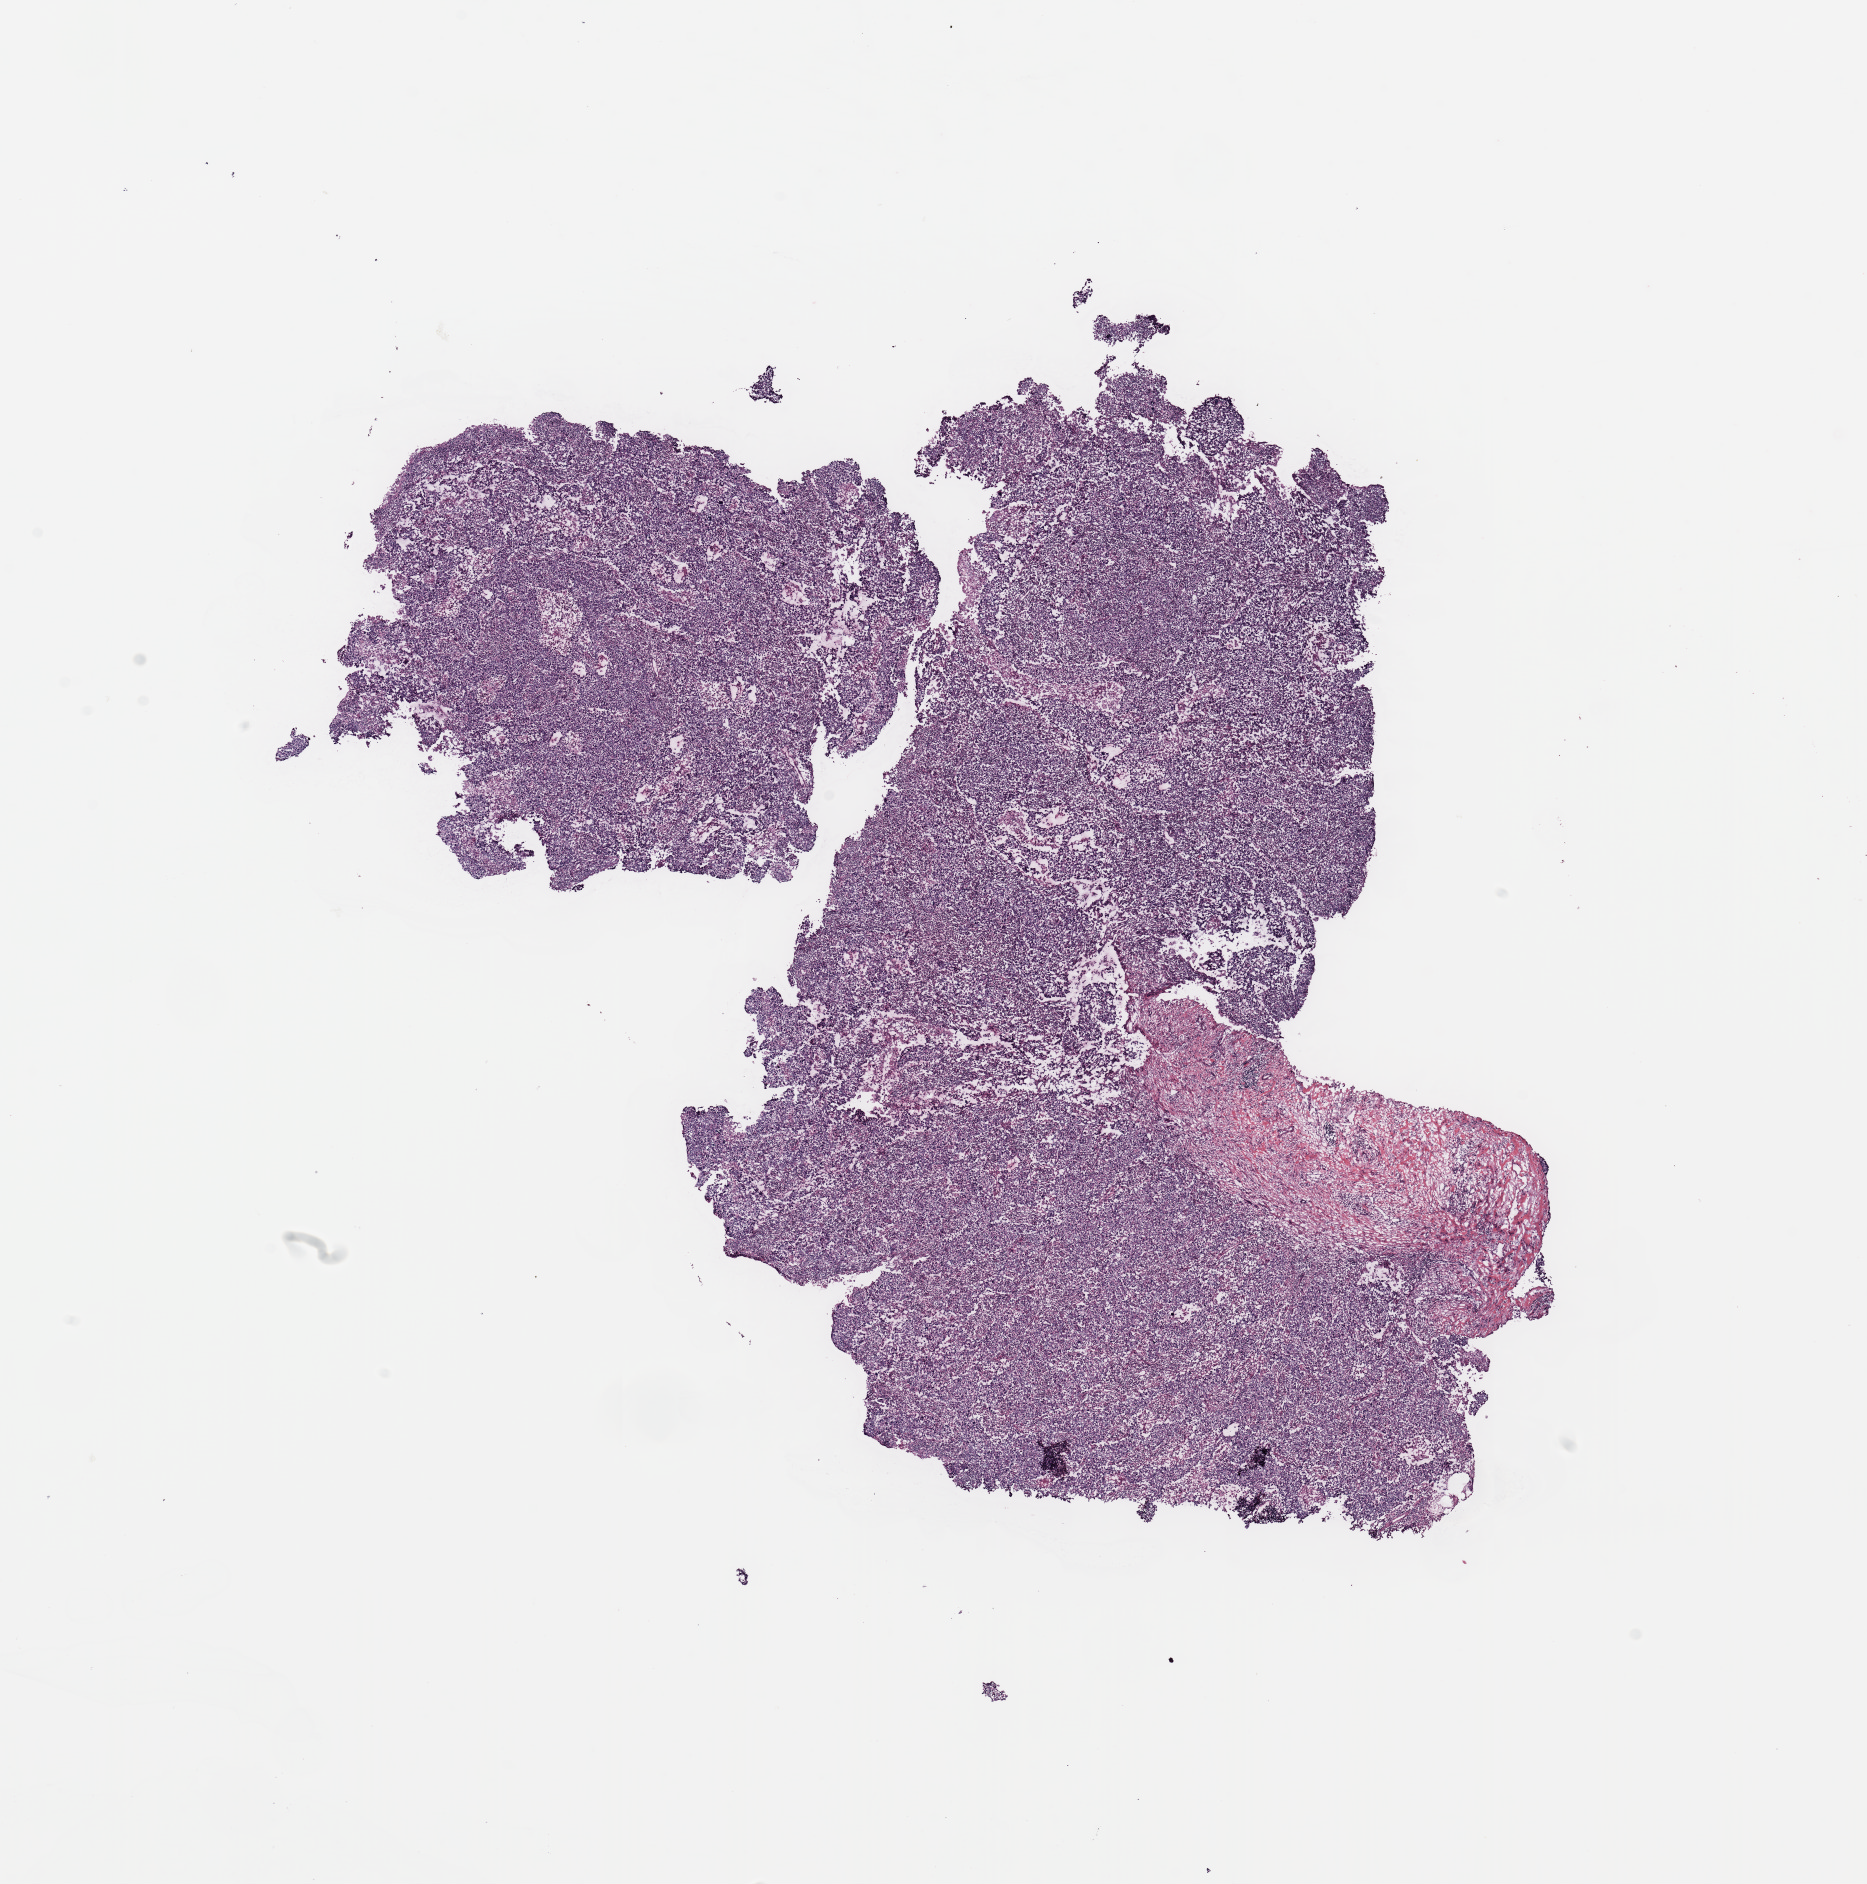
Digitized Hematoxylin and eosin (H&E) stained tissue section (whole slide), shown as a low-resolution overview of the whole scanned area (about 14.8 x 14.9 mm, from a 20x scan); breast, tissue type not recorded.
Patient diagnosis (cohort enrolment): breast cancer (breast).